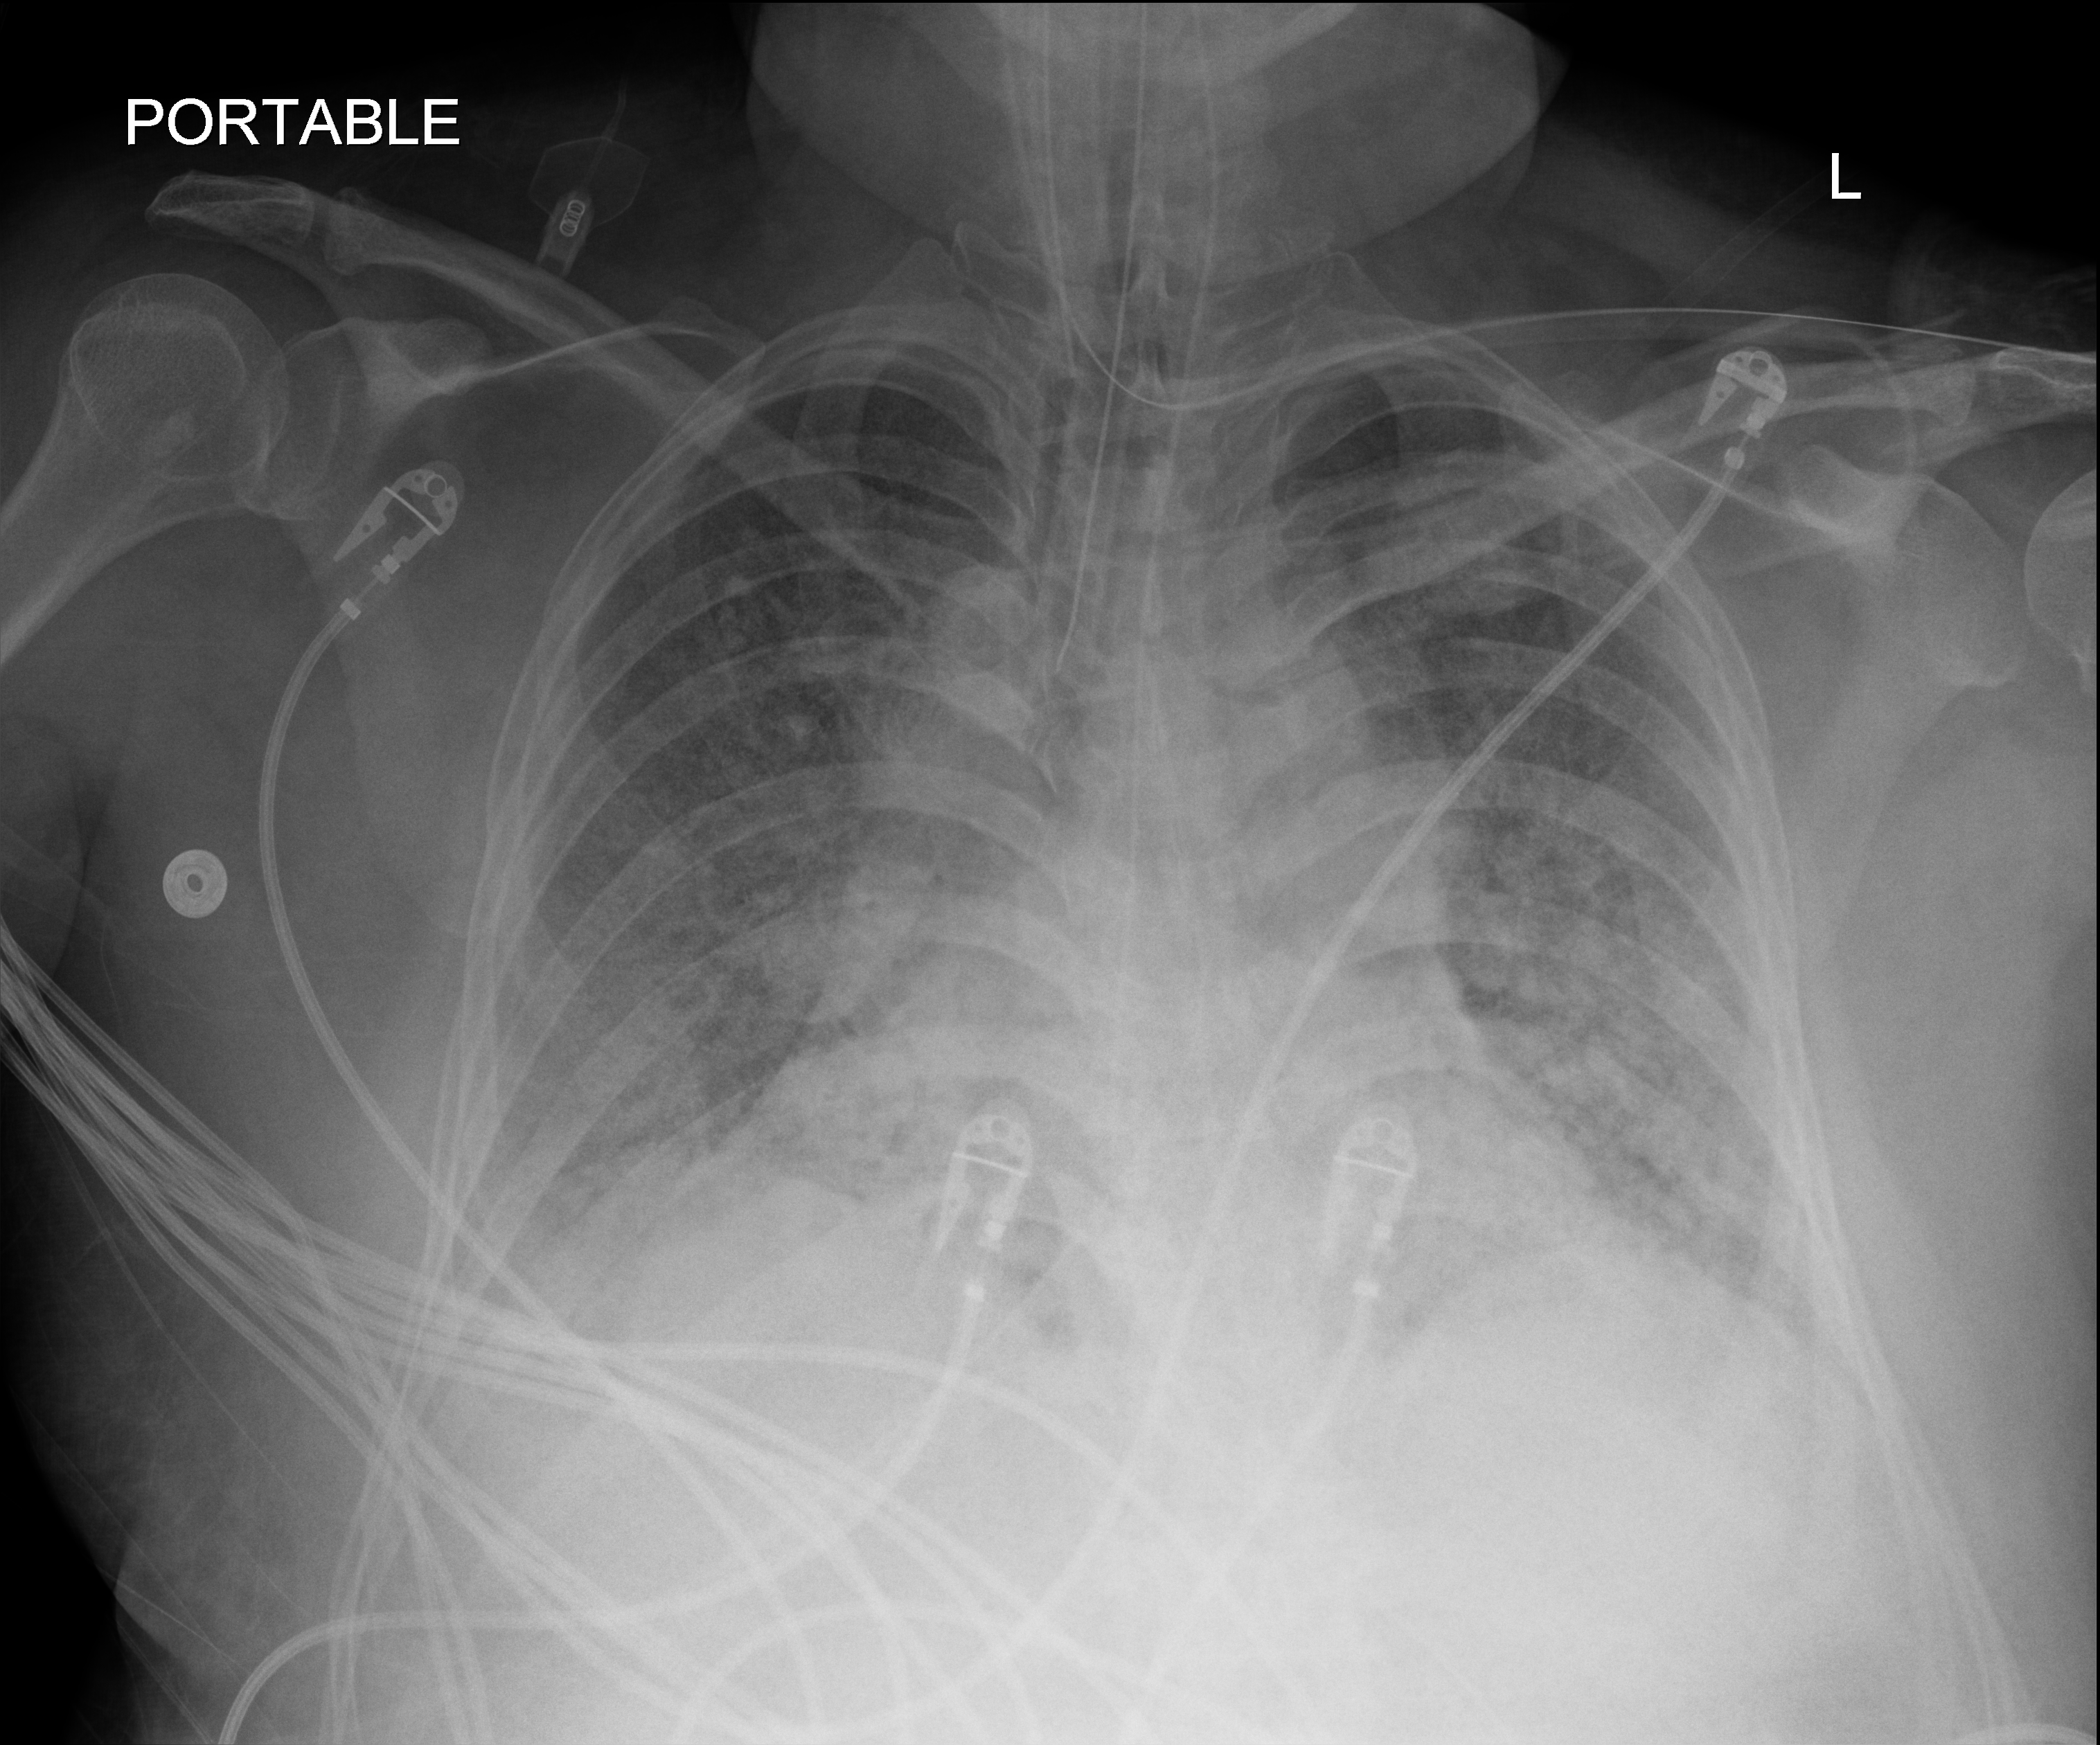
Chest X-ray (portable). Adult patient hospitalised with COVID-19, age 18–59 years.
Admission-level facts for this patient (not findings on this image; timing relative to this image not recorded): length of hospital stay: 48 days.